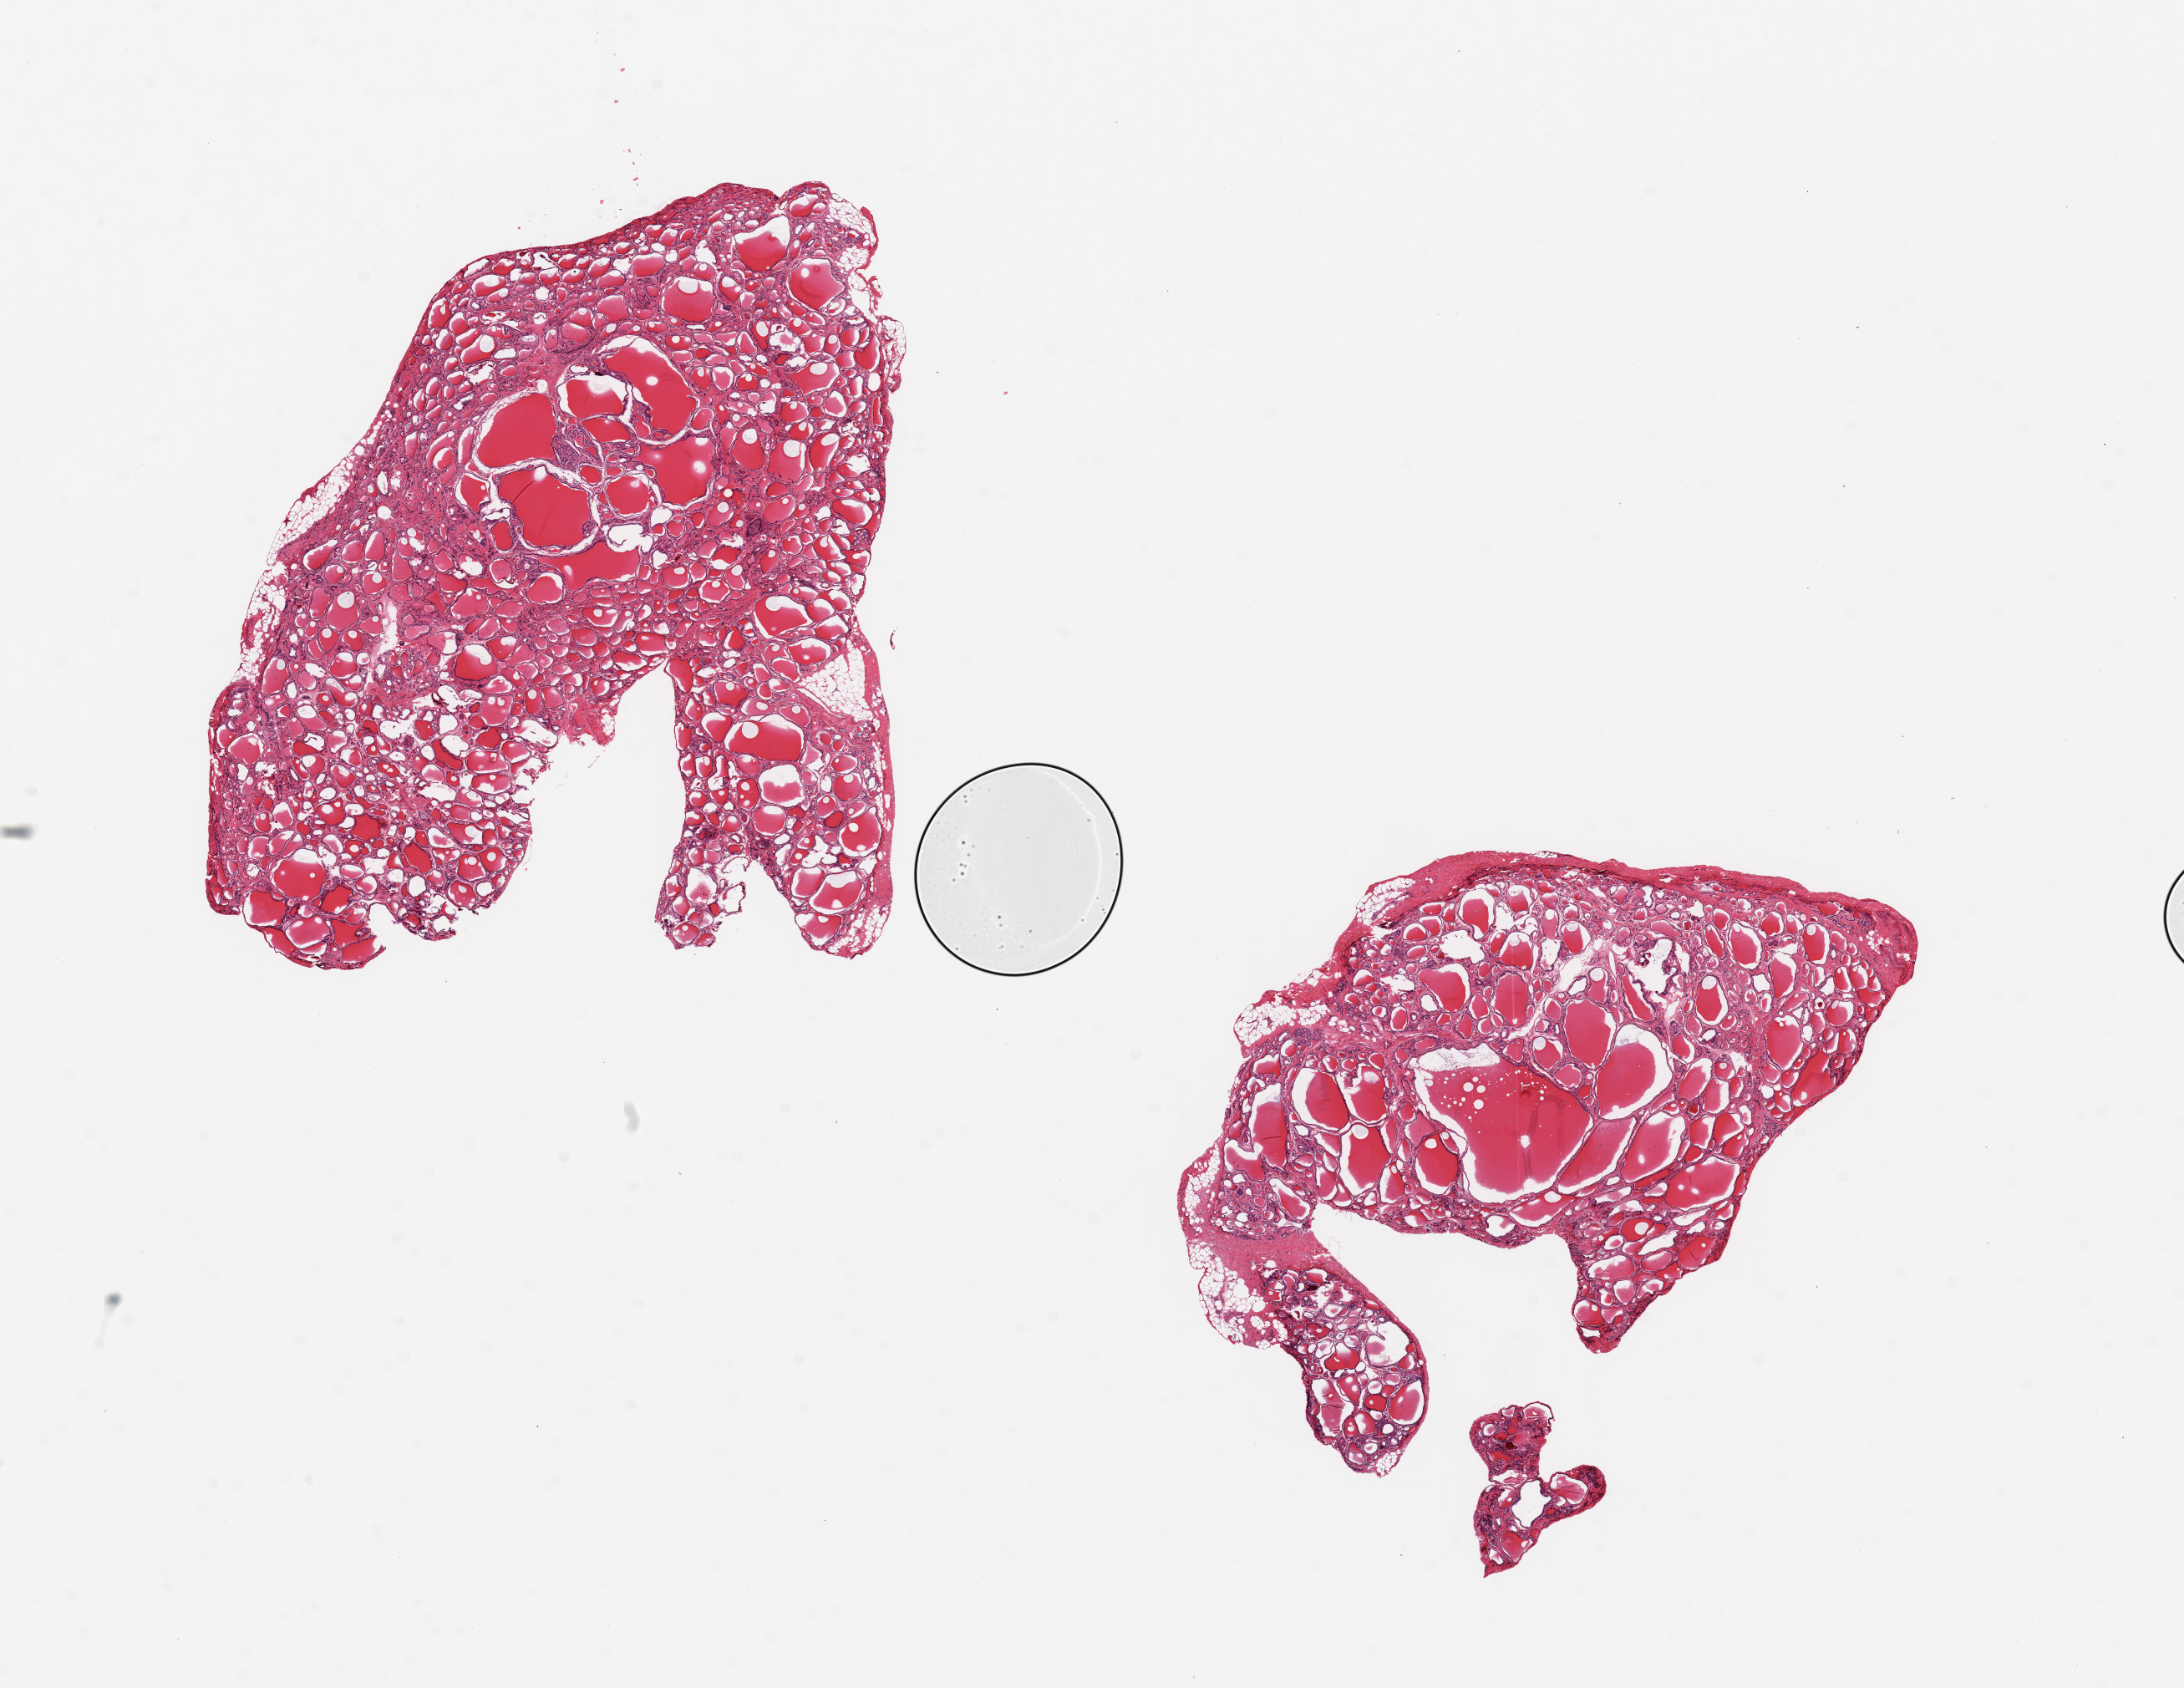
Whole-slide image, H&E stain, shown as a low-resolution overview of the whole scanned area (about 20.7 x 16.0 mm, from a 20x scan), PAXgene-fixed paraffin-embedded (PFPE) section, section of thyroid (target tissue), tissue donor sample. Male donor.
- pathologist's review note for this sample: 2 pieces ~8x4mm; Colloid nodules